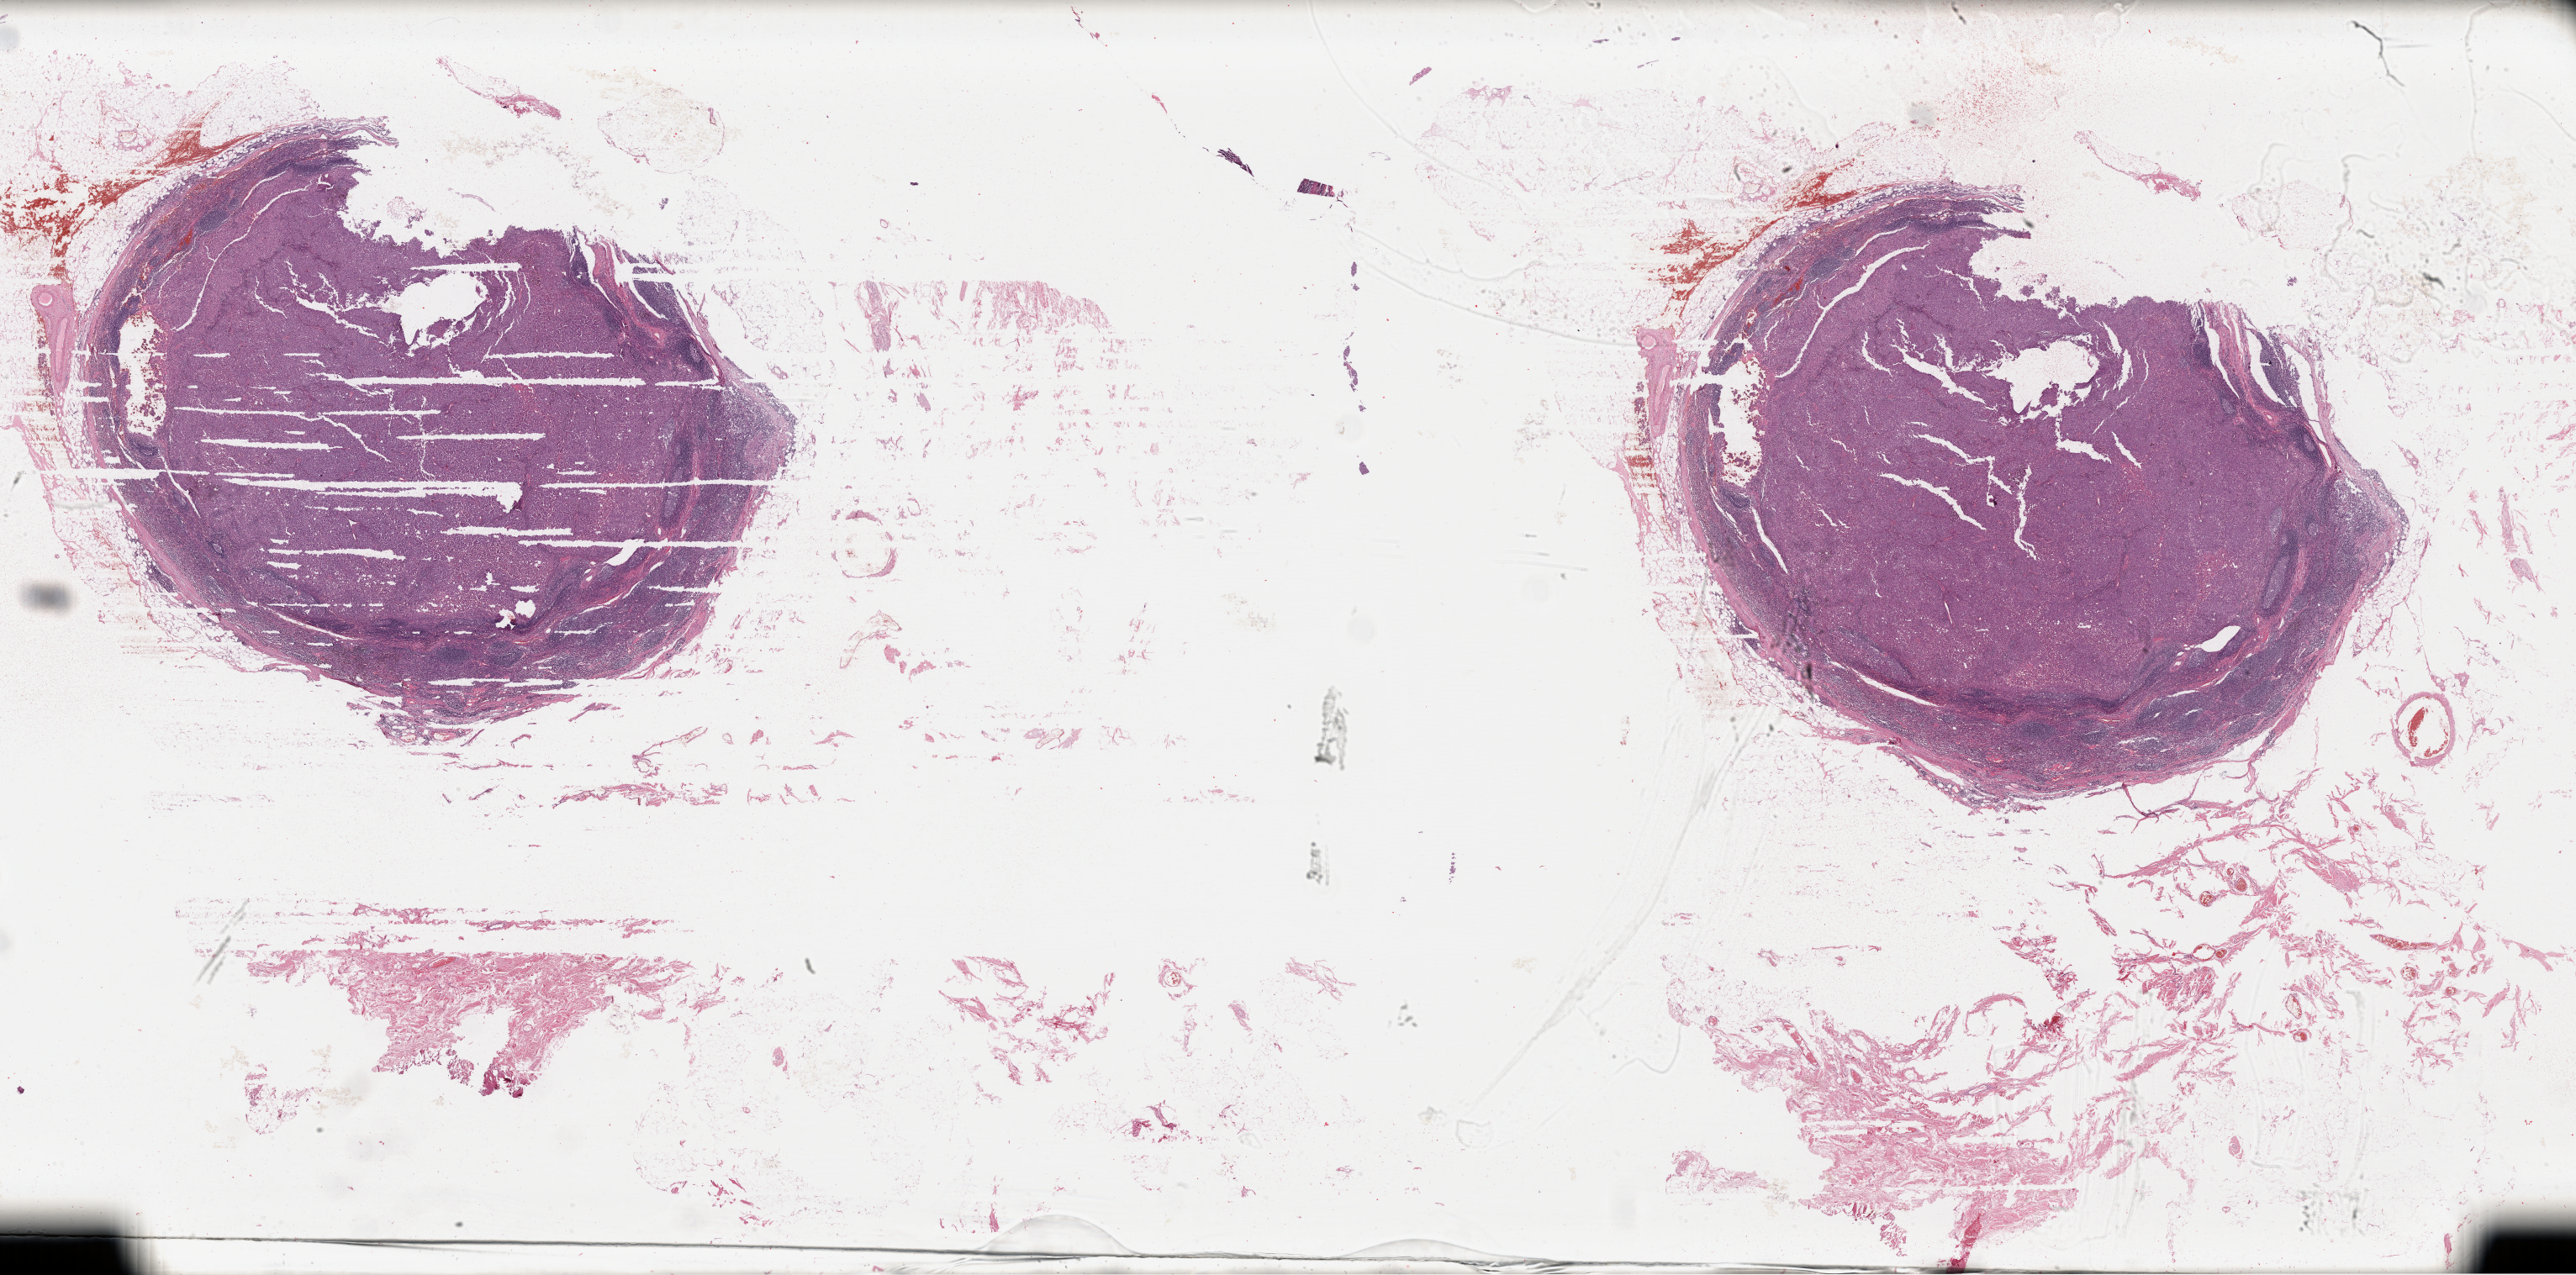
Digitized H&E tissue section (whole slide) — shown as a low-resolution overview of the whole scanned area (about 48.2 x 23.8 mm), formalin-fixed paraffin-embedded (FFPE) diagnostic section, metastatic tumour sample, sampled site: lymph node. Male patient; age at initial diagnosis 65 years.
This section: metastatic tumour tissue. Patient diagnosis: Malignant melanoma, NOS.